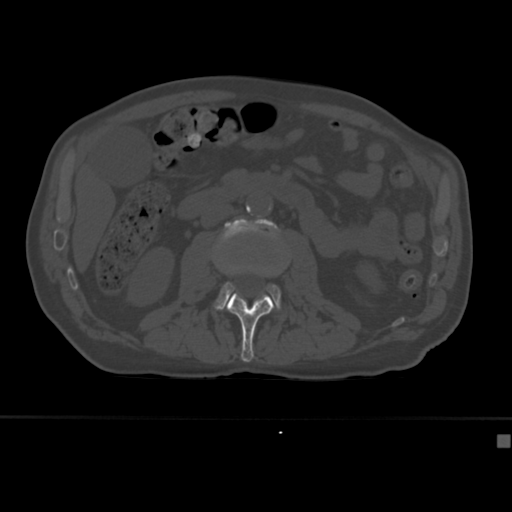
CT including the spine, one axial slice. Position 140 of 430 along the scan axis. 120 kVp. Bone window (W 1800 / L 400 HU). 512 × 512 image matrix, field of view 337 × 337 mm. Male patient, age 64 years. Case-level facts recorded for this patient, not image findings: primary cancer: uterus; vertebrae with lytic lesions (as recorded): T1, T4, T5, T7, L5.
Outlined on this slice (semi-automatically segmented with operator editing):
- L2 vertebra: box from (x=226, y=293) to (x=274, y=362) px
- L3 vertebra: (x=214, y=218)–(x=280, y=310)